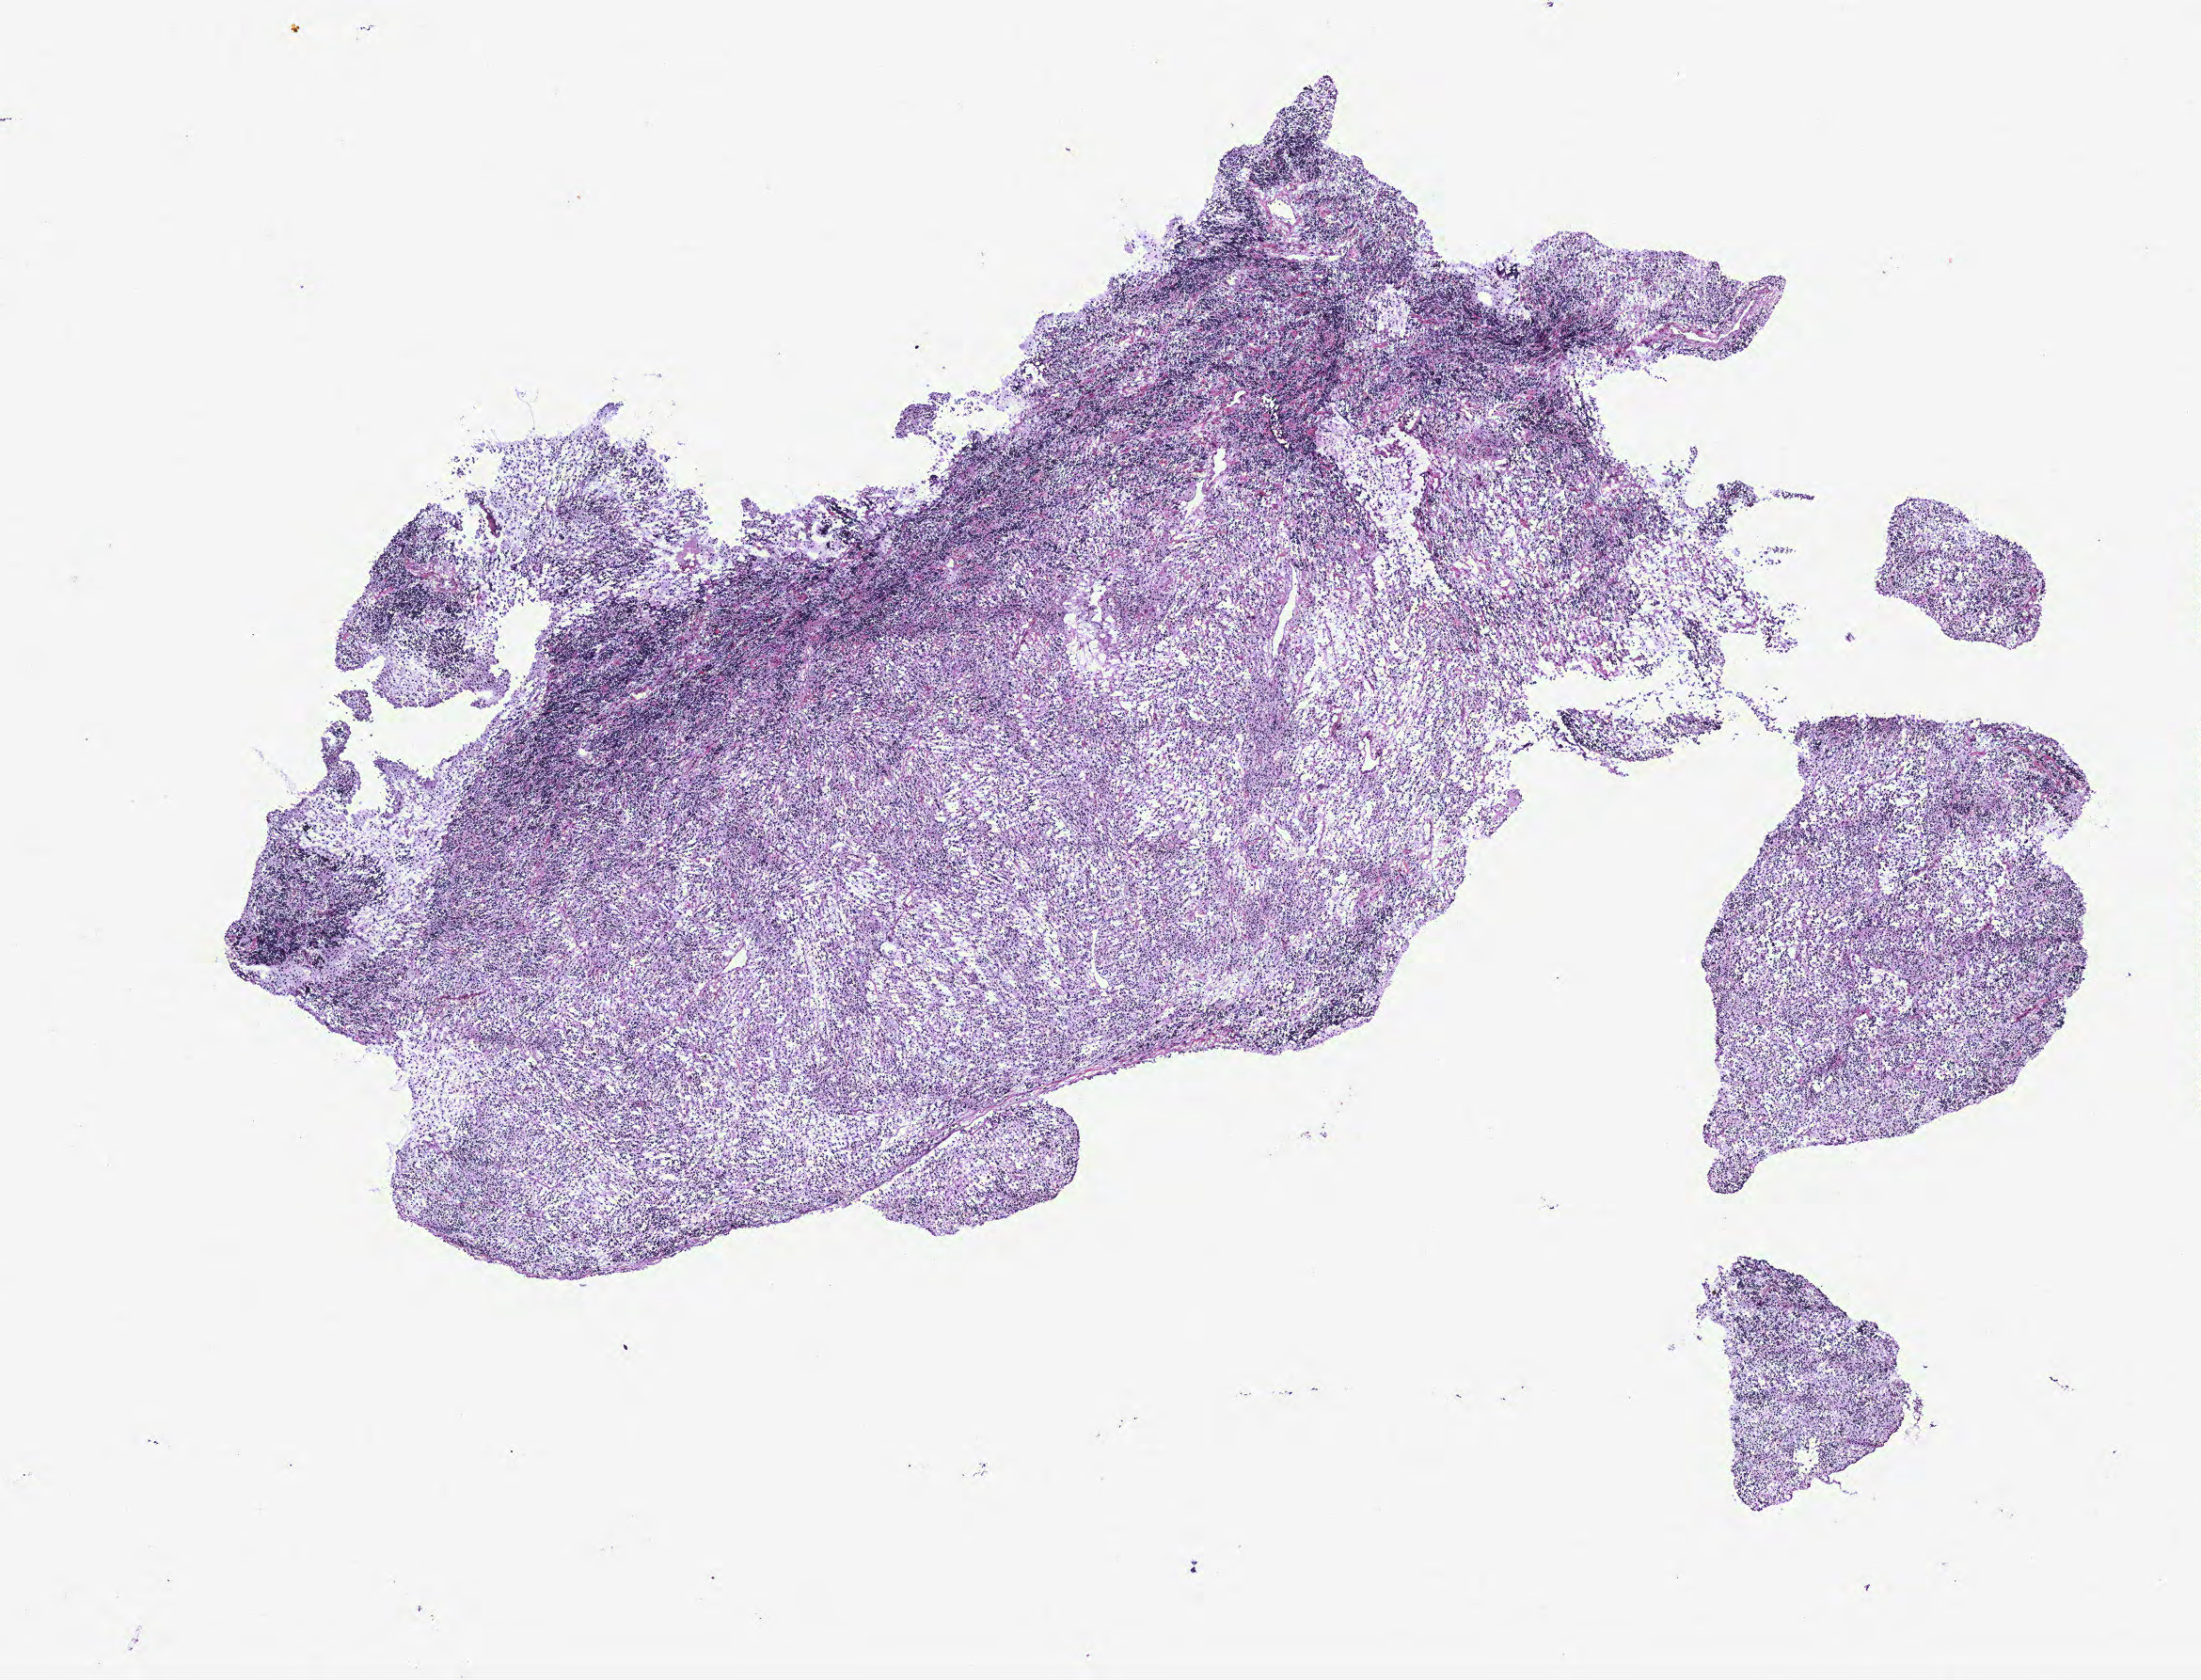
Digitized H&E tissue section (whole slide) — whole scanned area (about 9.4 x 7.1 mm, slide scanned at 40x) shown as a low-resolution overview. Ovary, tumour tissue. Female, 65 y/o.
Diagnosis: Serous adenocarcinoma, NOS. Primary tumour site (as recorded): ovary.